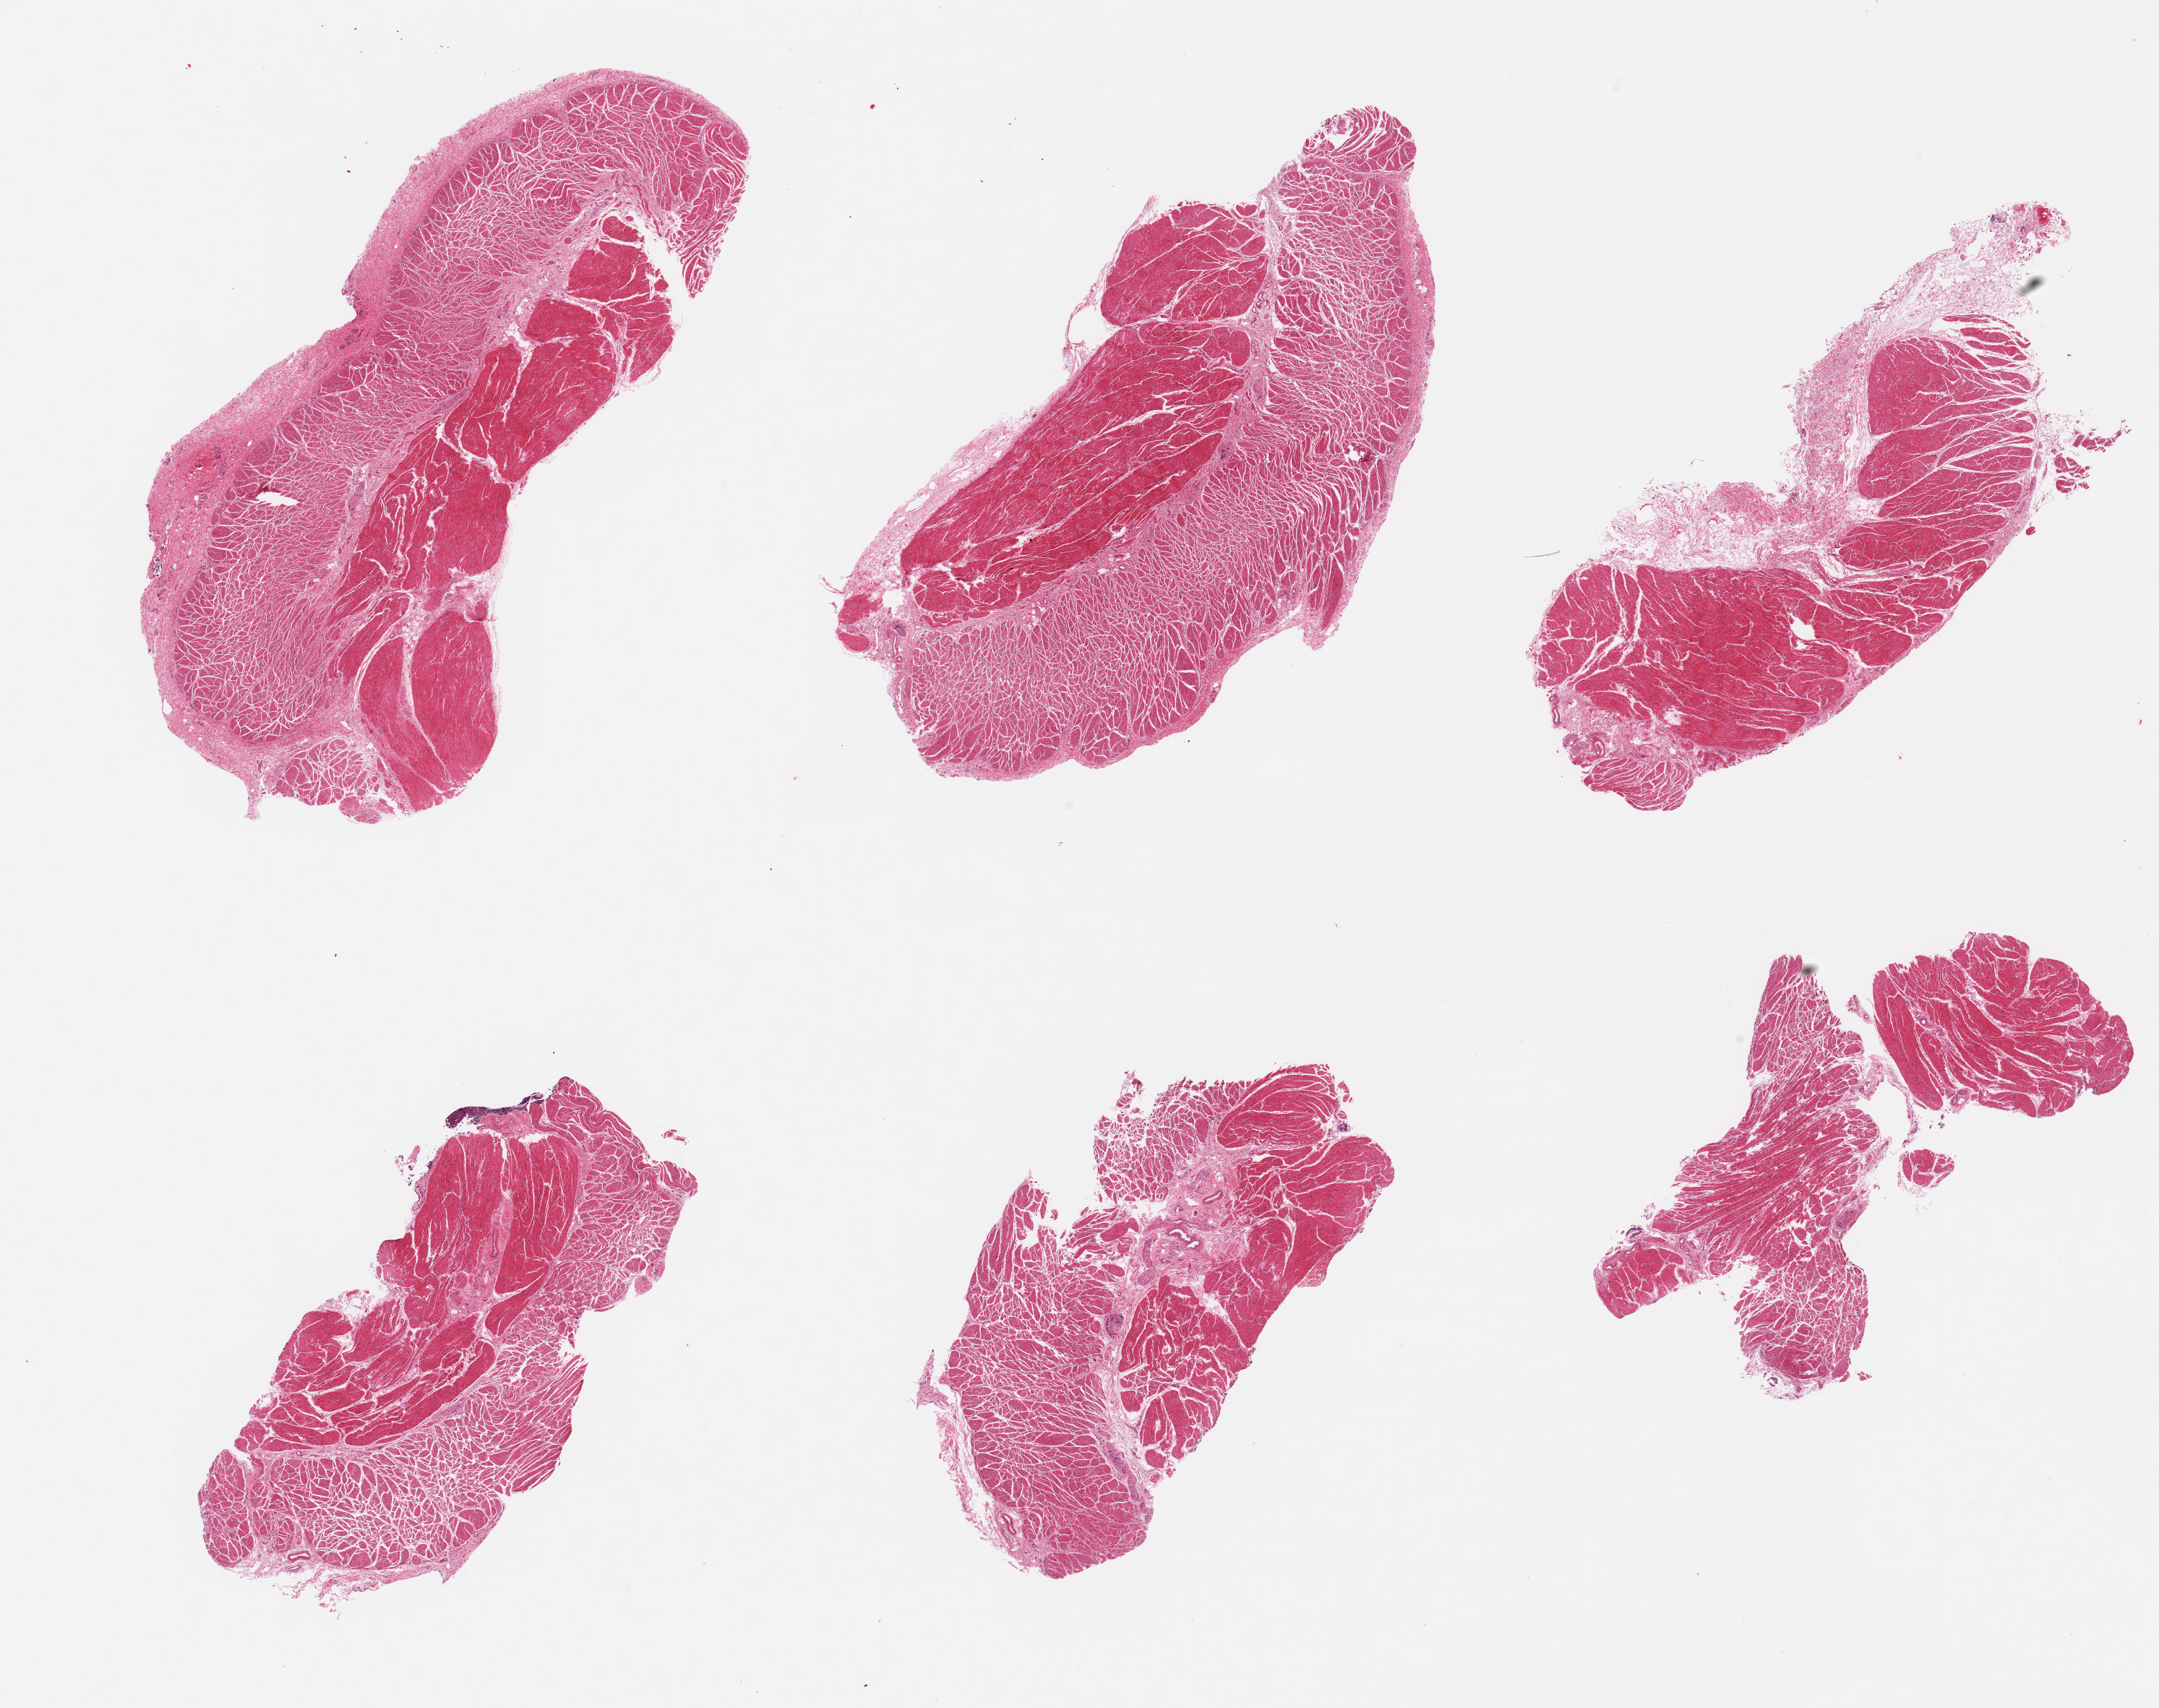
Whole-slide image, H&E stain — a low-resolution overview of the entire scanned area, about 23.6 x 18.7 mm (slide scanned at 20x). PAXgene-fixed paraffin-embedded (PFPE) section. Target tissue: esophageal muscle. Donor tissue sample.
* review note (as recorded): 6 pieces, confirmed target muscularis, adherent tags of fibroadipose tissue up to ~1mm